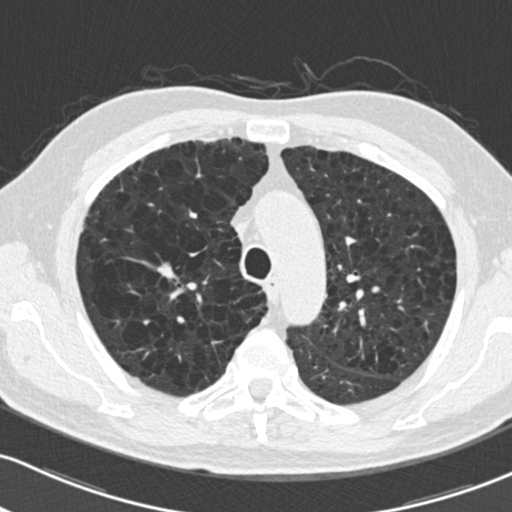
Chest CT (low-dose screening protocol), one axial image, second annual screen, lung window (W 1500 / L -600 HU), 2 mm slice thickness, 120 kVp, slice 51 of 204 in the series, 512 × 512 image matrix, field of view 318 × 318 mm. Male, age 73 years at enrolment. Current smoker at enrolment.
Lesion marked by an expert reader, box from (x=150, y=256) to (x=193, y=289) px. Reader record for this screening exam (exam-level; its link to the box is not recorded): non-calcified nodule or mass ≥4 mm, right upper lobe, 10 × 9 mm, smooth margins, soft tissue attenuation, pre-existing on the prior screen: yes; interval growth: yes. Official screen result: positive, other. Later outcome: lung cancer diagnosed 51 days after this screen — squamous cell carcinoma, NOS, right upper lobe, stage IA (AJCC 6th edition), 10 mm at pathology.